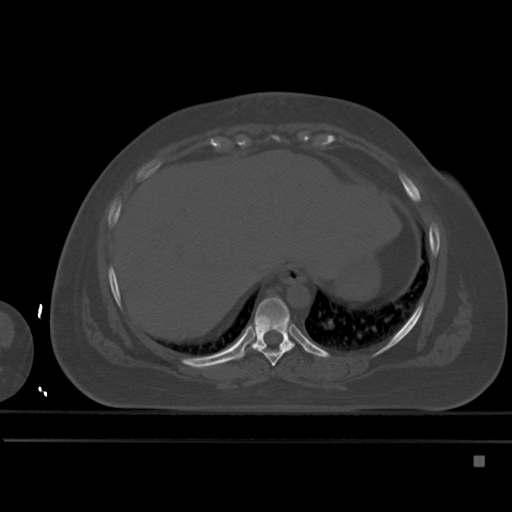
CT including the spine, one axial slice. Position 269 of 495 along the scan axis. Bone window (W 1800 / L 400 HU). 1.5 mm slice thickness. 512 × 512 image matrix, field of view 404 × 404 mm. Patient: female, 33 years. Case-level facts recorded for this patient, not image findings: primary cancer: breast; vertebrae with lytic lesions (as recorded): T1.
Outlined on this slice (semi-automatically segmented with operator editing):
- T8 vertebra: box from (x=254, y=347) to (x=293, y=366) px
- T9 vertebra: (x=242, y=297)–(x=295, y=358)